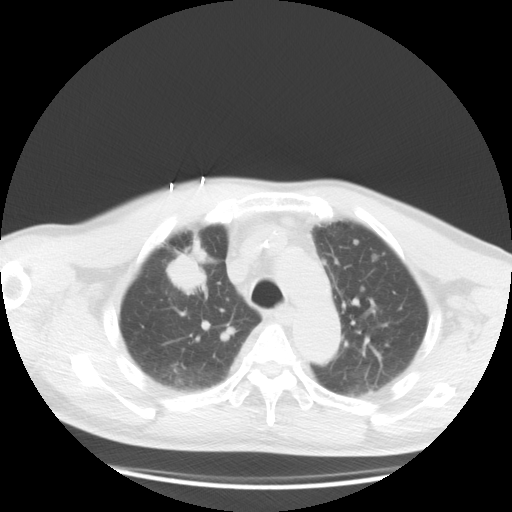
Chest CT, one axial slice; position 23 of 36 along the scan axis; reconstruction kernel STANDARD; 120 kVp; lung window (W 1500 / L -600 HU); 5 mm slice thickness; 512 × 512 image matrix, field of view 369 × 369 mm. Patient: male, 57 years. From the clinical record (not read from this slice): clinical TNM (as recorded): T2 N3 M1a.
Annotated regions visible in this slice (rectangle marked by the reading radiologist):
- lung tumour (recorded histology: adenocarcinoma): bounding box [x1, y1, x2, y2] px = [166, 237, 207, 295]